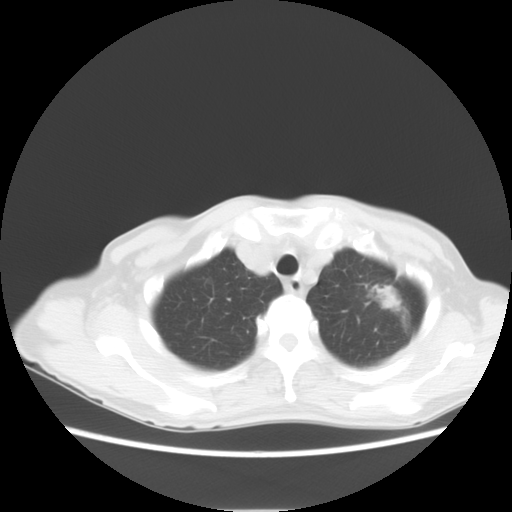
Chest CT, one axial slice; position 9 of 11 along the scan axis; lung window (W 1500 / L -600 HU); 512 × 512 image matrix, field of view 350 × 350 mm. Female patient, age 71 years. From the clinical record (not read from this slice): clinical TNM (as recorded): T2 N0 M0.
Outlined on this slice (rectangle marked by the reading radiologist):
- lung tumour (recorded histology: adenocarcinoma): bounding box (x1, y1, x2, y2) in pixels: (378, 283, 398, 313)